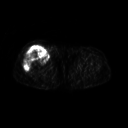
FDG PET of an extremity soft-tissue mass (from a PET/CT study), one axial slice; slice 241 of 311 in the series (ordered by position); 3.27 mm slice thickness; 128 × 128 image matrix. Female patient, age 57 years. Case-level facts recorded for this patient, not image findings: histological type: pleiomorphic undifferentiated sarcoma; grade: high; site of the primary tumour: right quadricep.
Structures marked on this image (expert contour drawn on MRI and transferred to this co-registered scan by the dataset authors):
- tumour plus oedema (research contour): bounding box (x1, y1, x2, y2) in pixels: (24, 47, 48, 71)
- tumour (research contour): (24, 47, 48, 71)